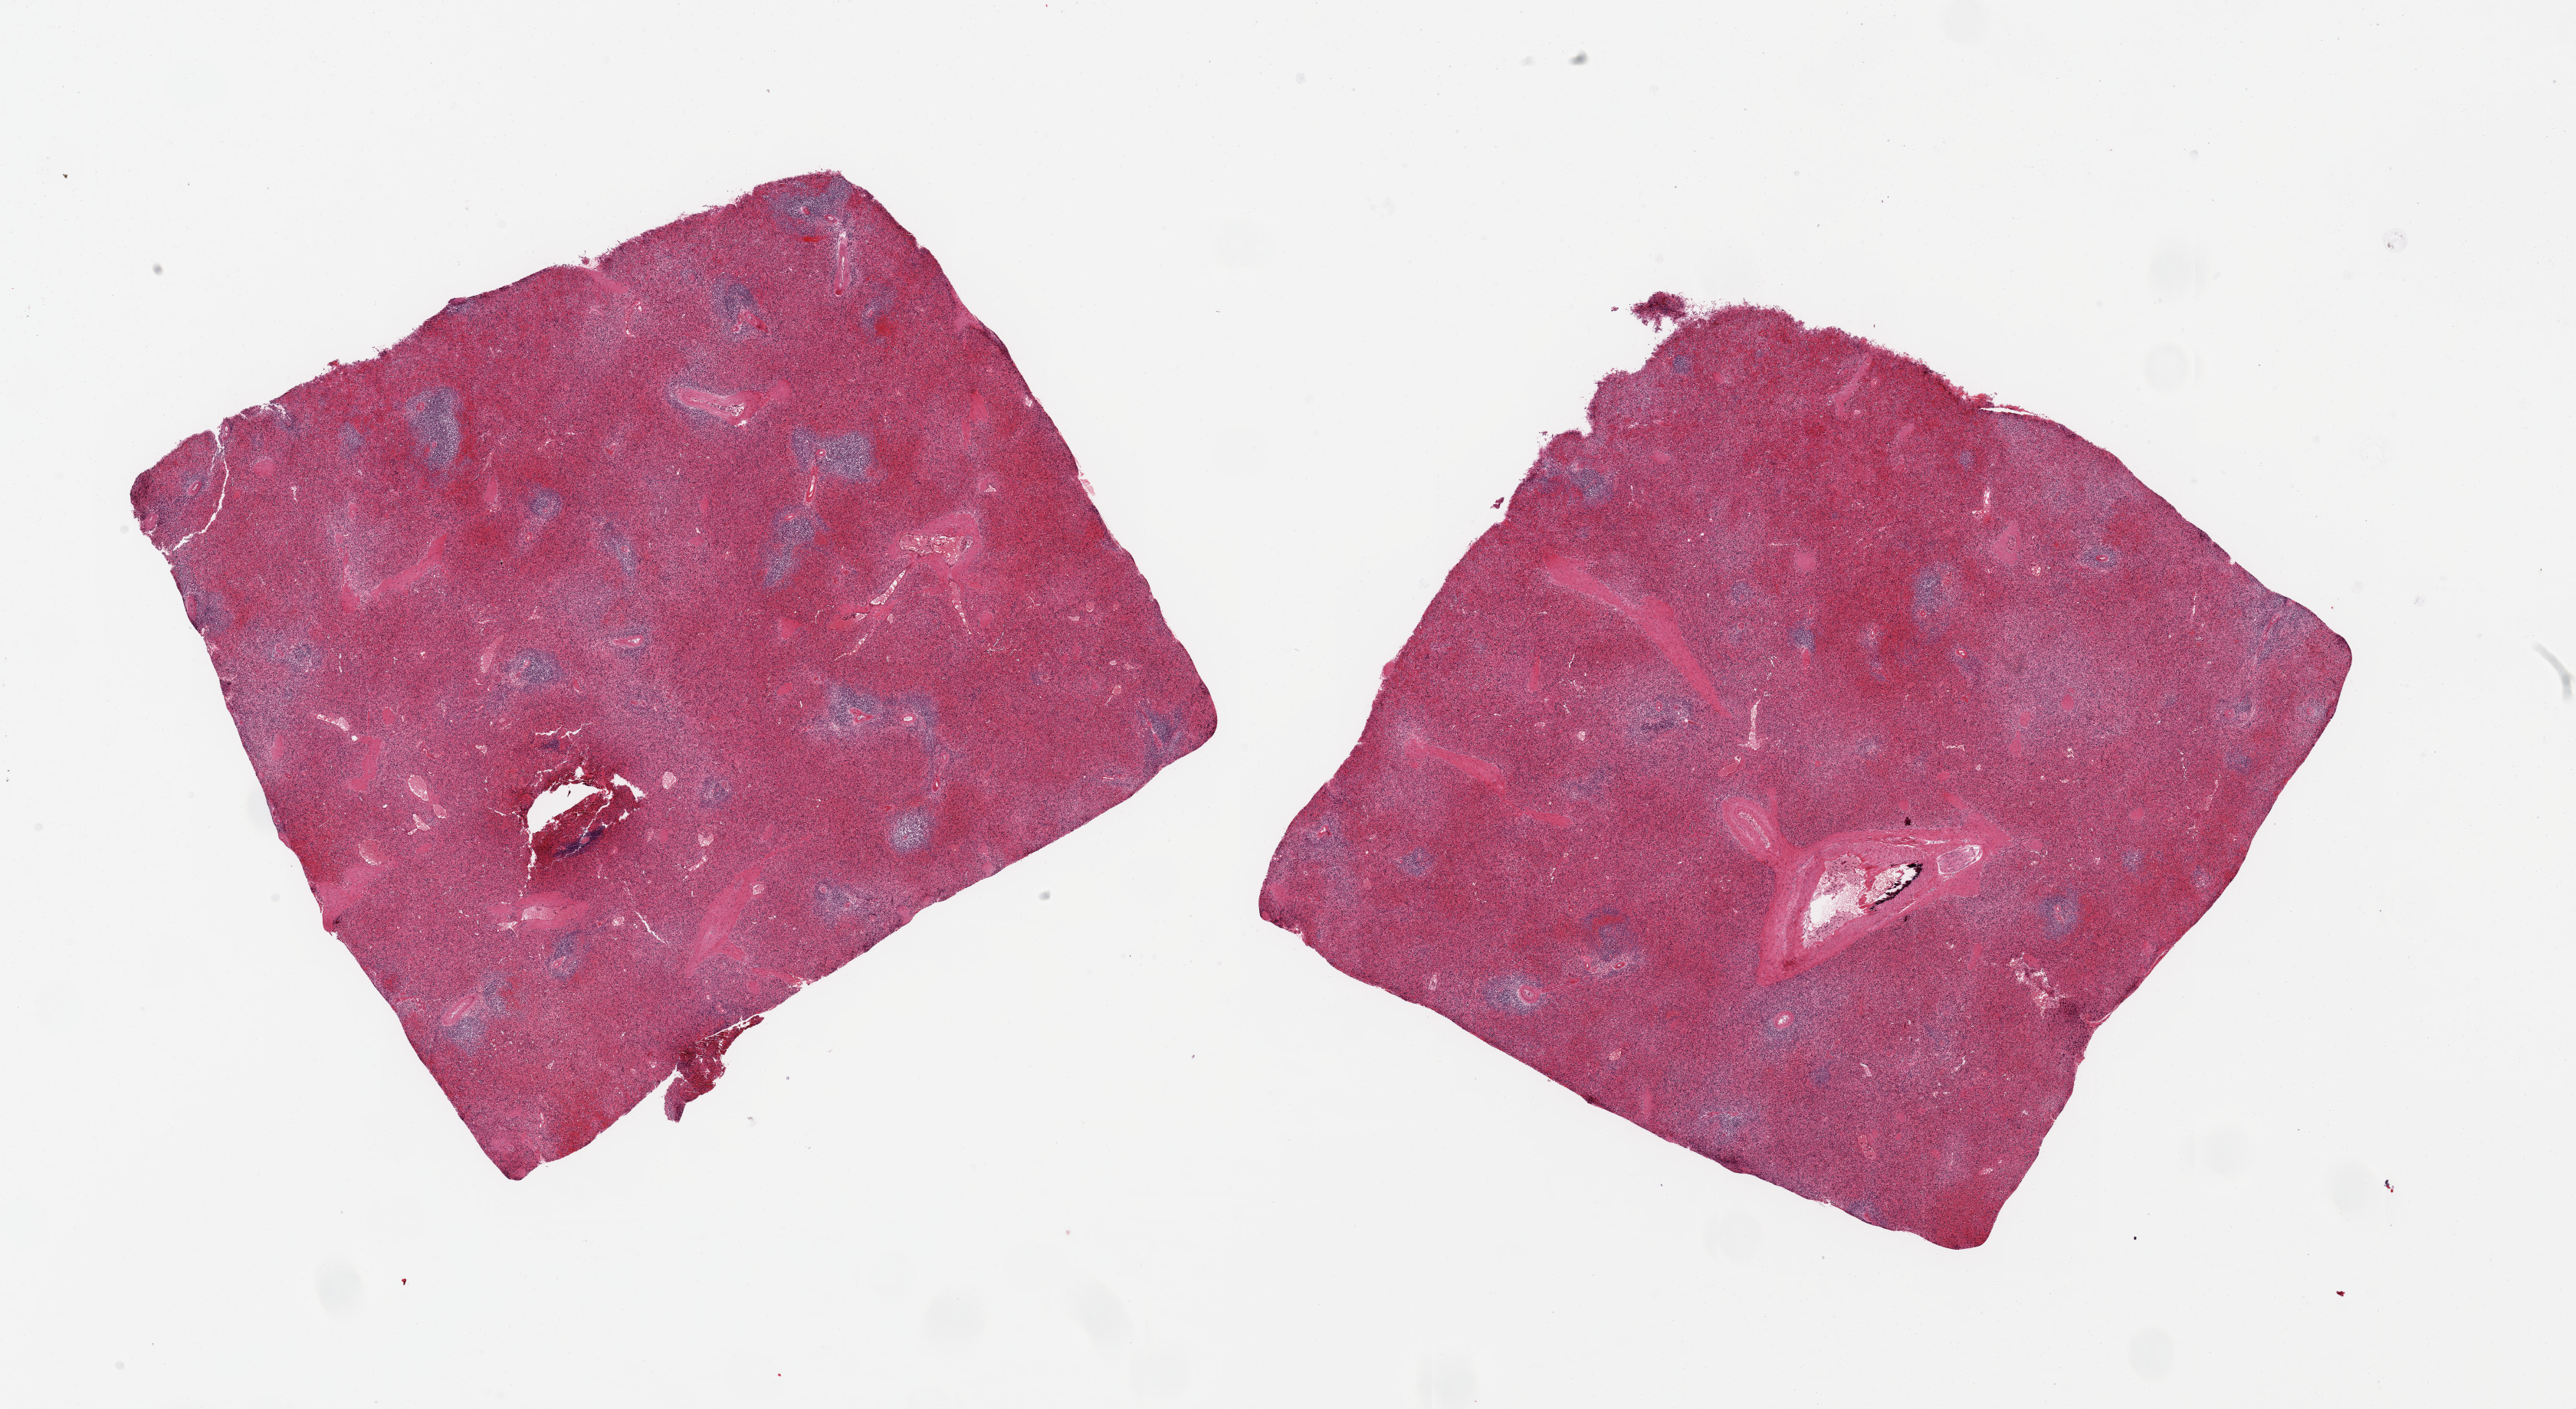
Digitized hematoxylin and eosin (H&E)-stained section — shown as a low-resolution overview of the whole scanned area (about 26.6 x 14.5 mm, acquisition: 20x scan); PAXgene-fixed, paraffin-embedded tissue; target tissue: spleen; donor tissue sample. Donor sex: female.
Review note (as recorded): 2 pieces, congestion, advanced autolysis.